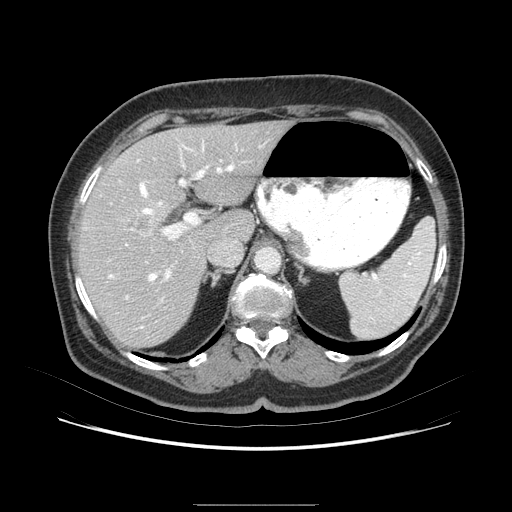
Contrast-enhanced abdominal CT (liver protocol), one axial slice. Slice 50 of 79 in the series (ordered by position). 120 kVp. Soft-tissue window (W 400 / L 40 HU). 2.5 mm slice thickness. 512 × 512 image matrix. From the clinical record (not read from this slice): diagnosis: hepatocellular carcinoma (patient treated with transarterial chemoembolisation; whether this scan precedes or follows treatment is not stated here); TNM stage (as recorded): Stage-I; Child-Pugh class: A; tumour nodularity: uninodular.
Annotated regions visible in this slice (semi-automatically segmented with operator editing):
- liver parenchyma outside the tumour (the mass and vessels are separate outlines, so this box may not span the whole liver): bounding box <74,124,296,346> (left, top, right, bottom; pixels)
- liver vessels: <82,148,263,296>